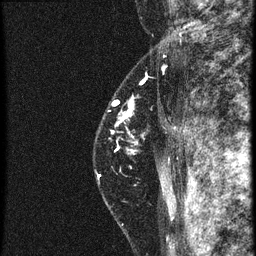
Breast MRI (dynamic contrast-enhanced), one sagittal slice. Position 47 of 60 along the scan axis. 4 images stored at this slice position (order not interpretable as contrast timing). 1.5 T. TE 4.2 ms, TR 20.4 ms. 256 × 256 image matrix, field of view 180 × 180 mm. Female patient, age 46 years. From the clinical record (not read from this slice): setting: breast cancer imaged before/during neoadjuvant chemotherapy; receptor status: triple-negative.
Structures marked on this image (semi-automatically segmented with operator editing):
- analysis volume of interest (the breast-tissue region the enhancement analysis was run in; not a lesion): bounding box [x1, y1, x2, y2] px = [92, 82, 181, 185]
- tumour enhancement mask (voxels above the 90 % enhancement threshold inside the analysis volume of interest): [98, 102, 133, 179]